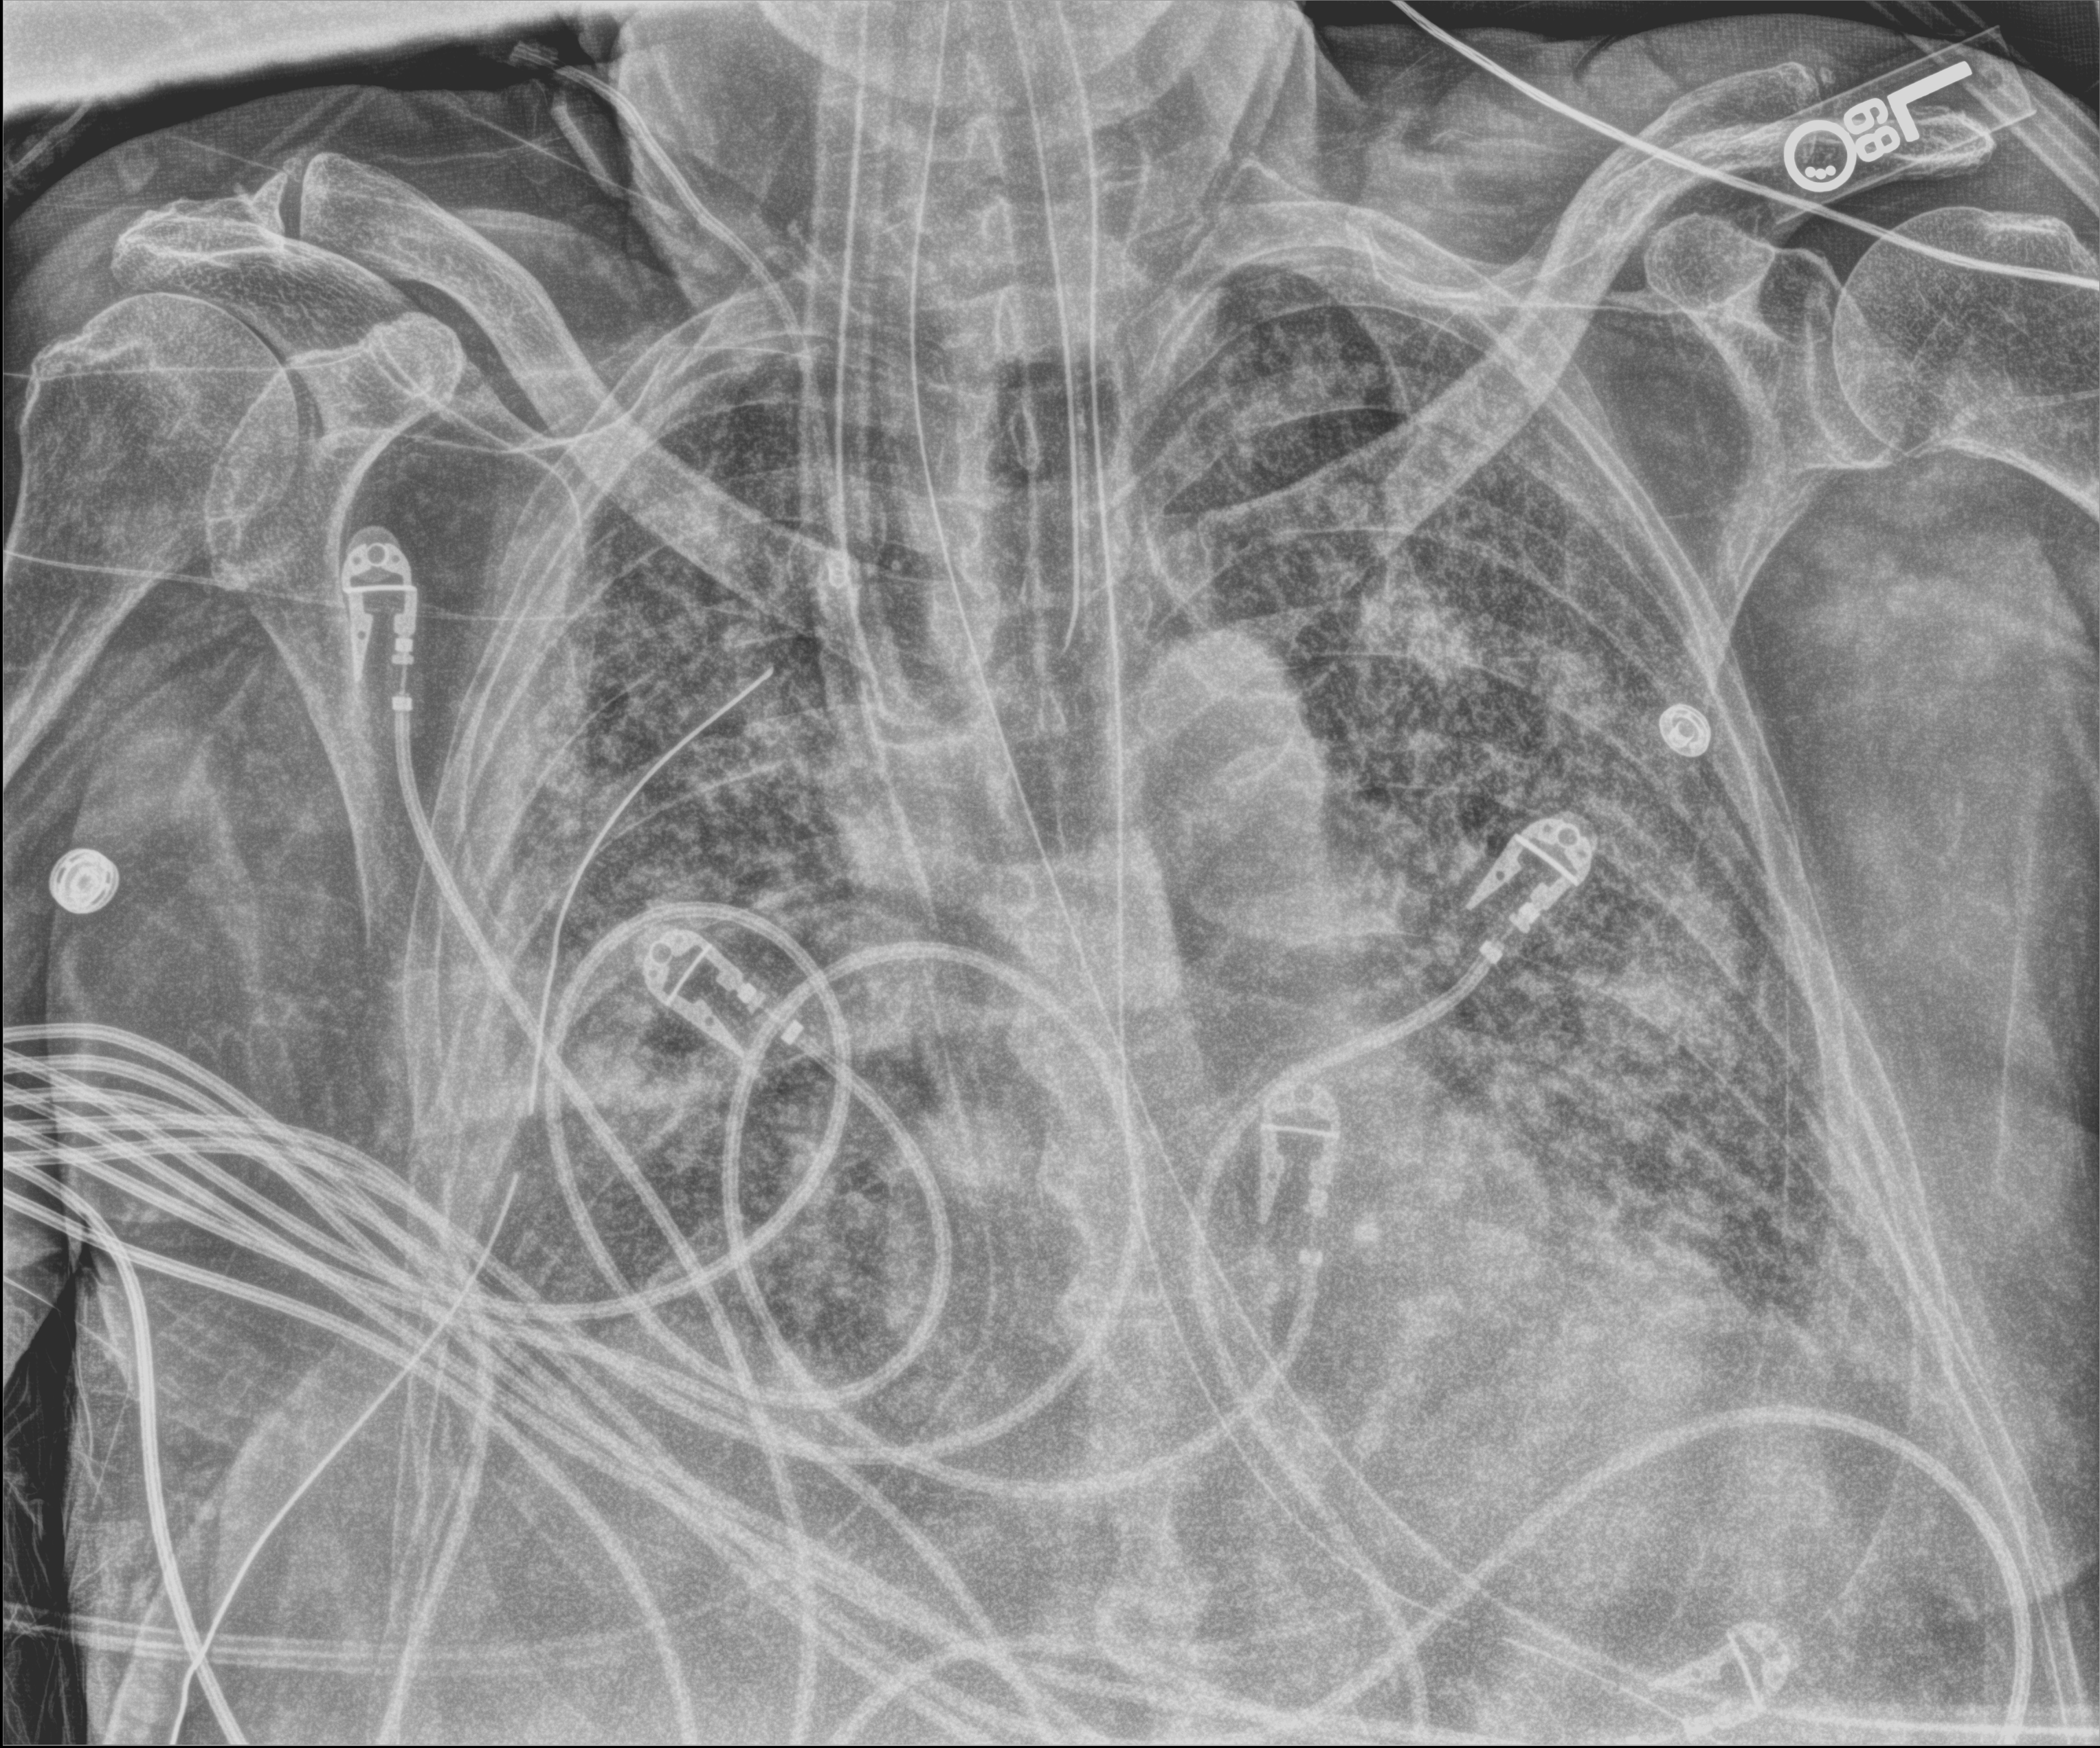
Chest X-ray (portable), anteroposterior (AP) projection. Patient hospitalised with COVID-19; male, aged 75–90 years.
Admission-level facts for this patient (not findings on this image; timing relative to this image not recorded): chronic kidney disease (admission record): no.